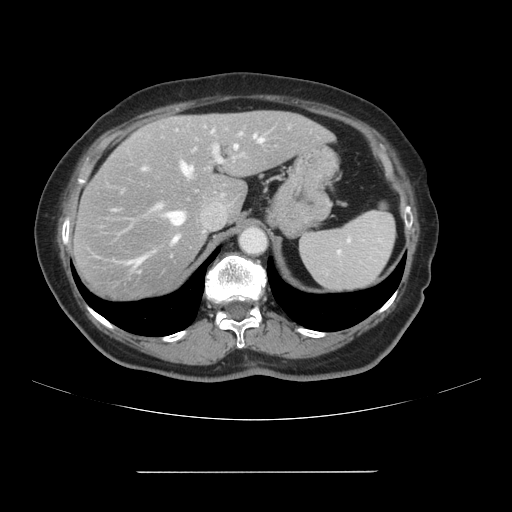
Contrast-enhanced abdominal CT, one axial slice; intravenous contrast given; soft-tissue window (W 400 / L 40 HU); 2.5 mm slice thickness; 512 × 512 image matrix, field of view 400 × 400 mm. Female patient, age 74 years. From the clinical record (not read from this slice): diagnosis: colorectal cancer liver metastases, imaged before liver resection; multiple liver metastases: yes.
Annotated regions visible in this slice (manually delineated by an expert):
- hepatic veins: bounding box (x1, y1, x2, y2) in pixels: (111, 134, 264, 273)
- liver: (74, 111, 332, 302)
- planned liver remnant (the part of the liver to remain after resection): (155, 112, 332, 218)
- portal vein (with intrahepatic branches): (144, 134, 242, 208)